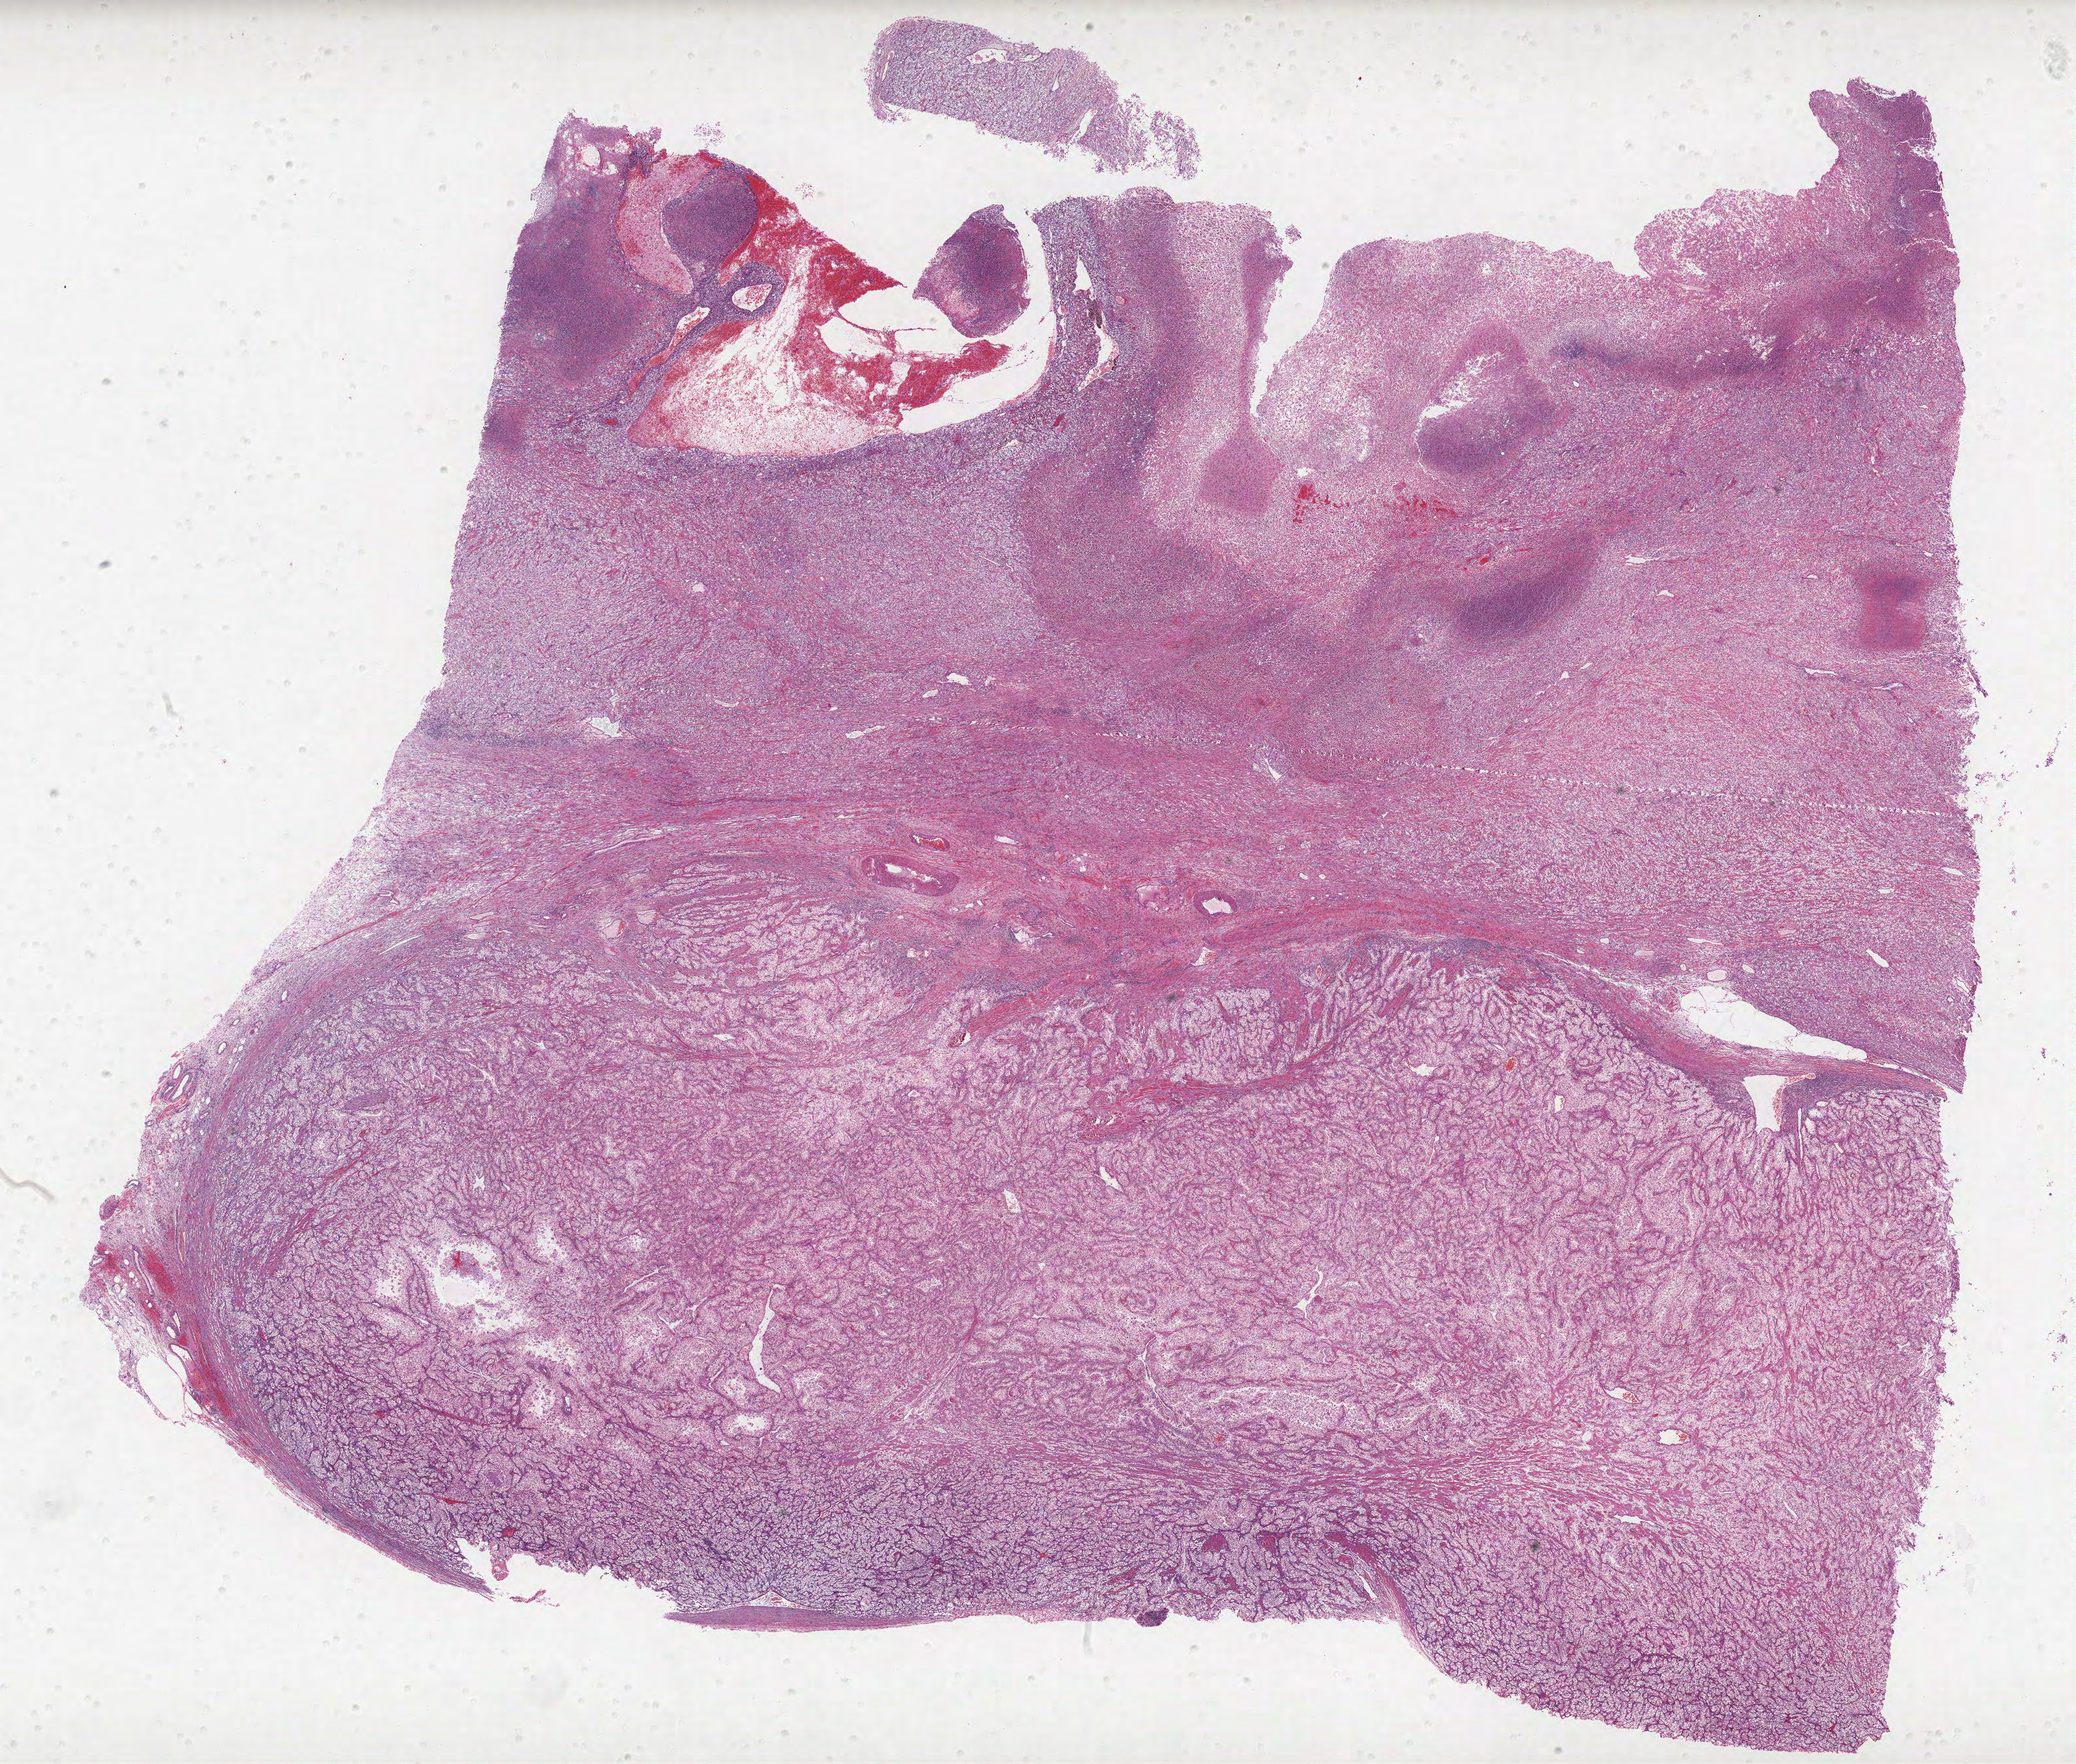
Digitized H&E tissue section (whole slide) — low-resolution overview of the scanned area, about 25.2 x 21.4 mm (from a 40x scan). Formalin-fixed paraffin-embedded (FFPE) diagnostic section. Sample: primary tumour, kidney. Patient: male, age at initial diagnosis 63 years. Histologic grade: G4 (undifferentiated).
- diagnosis: Clear cell adenocarcinoma, NOS
- AJCC pathologic stage: III